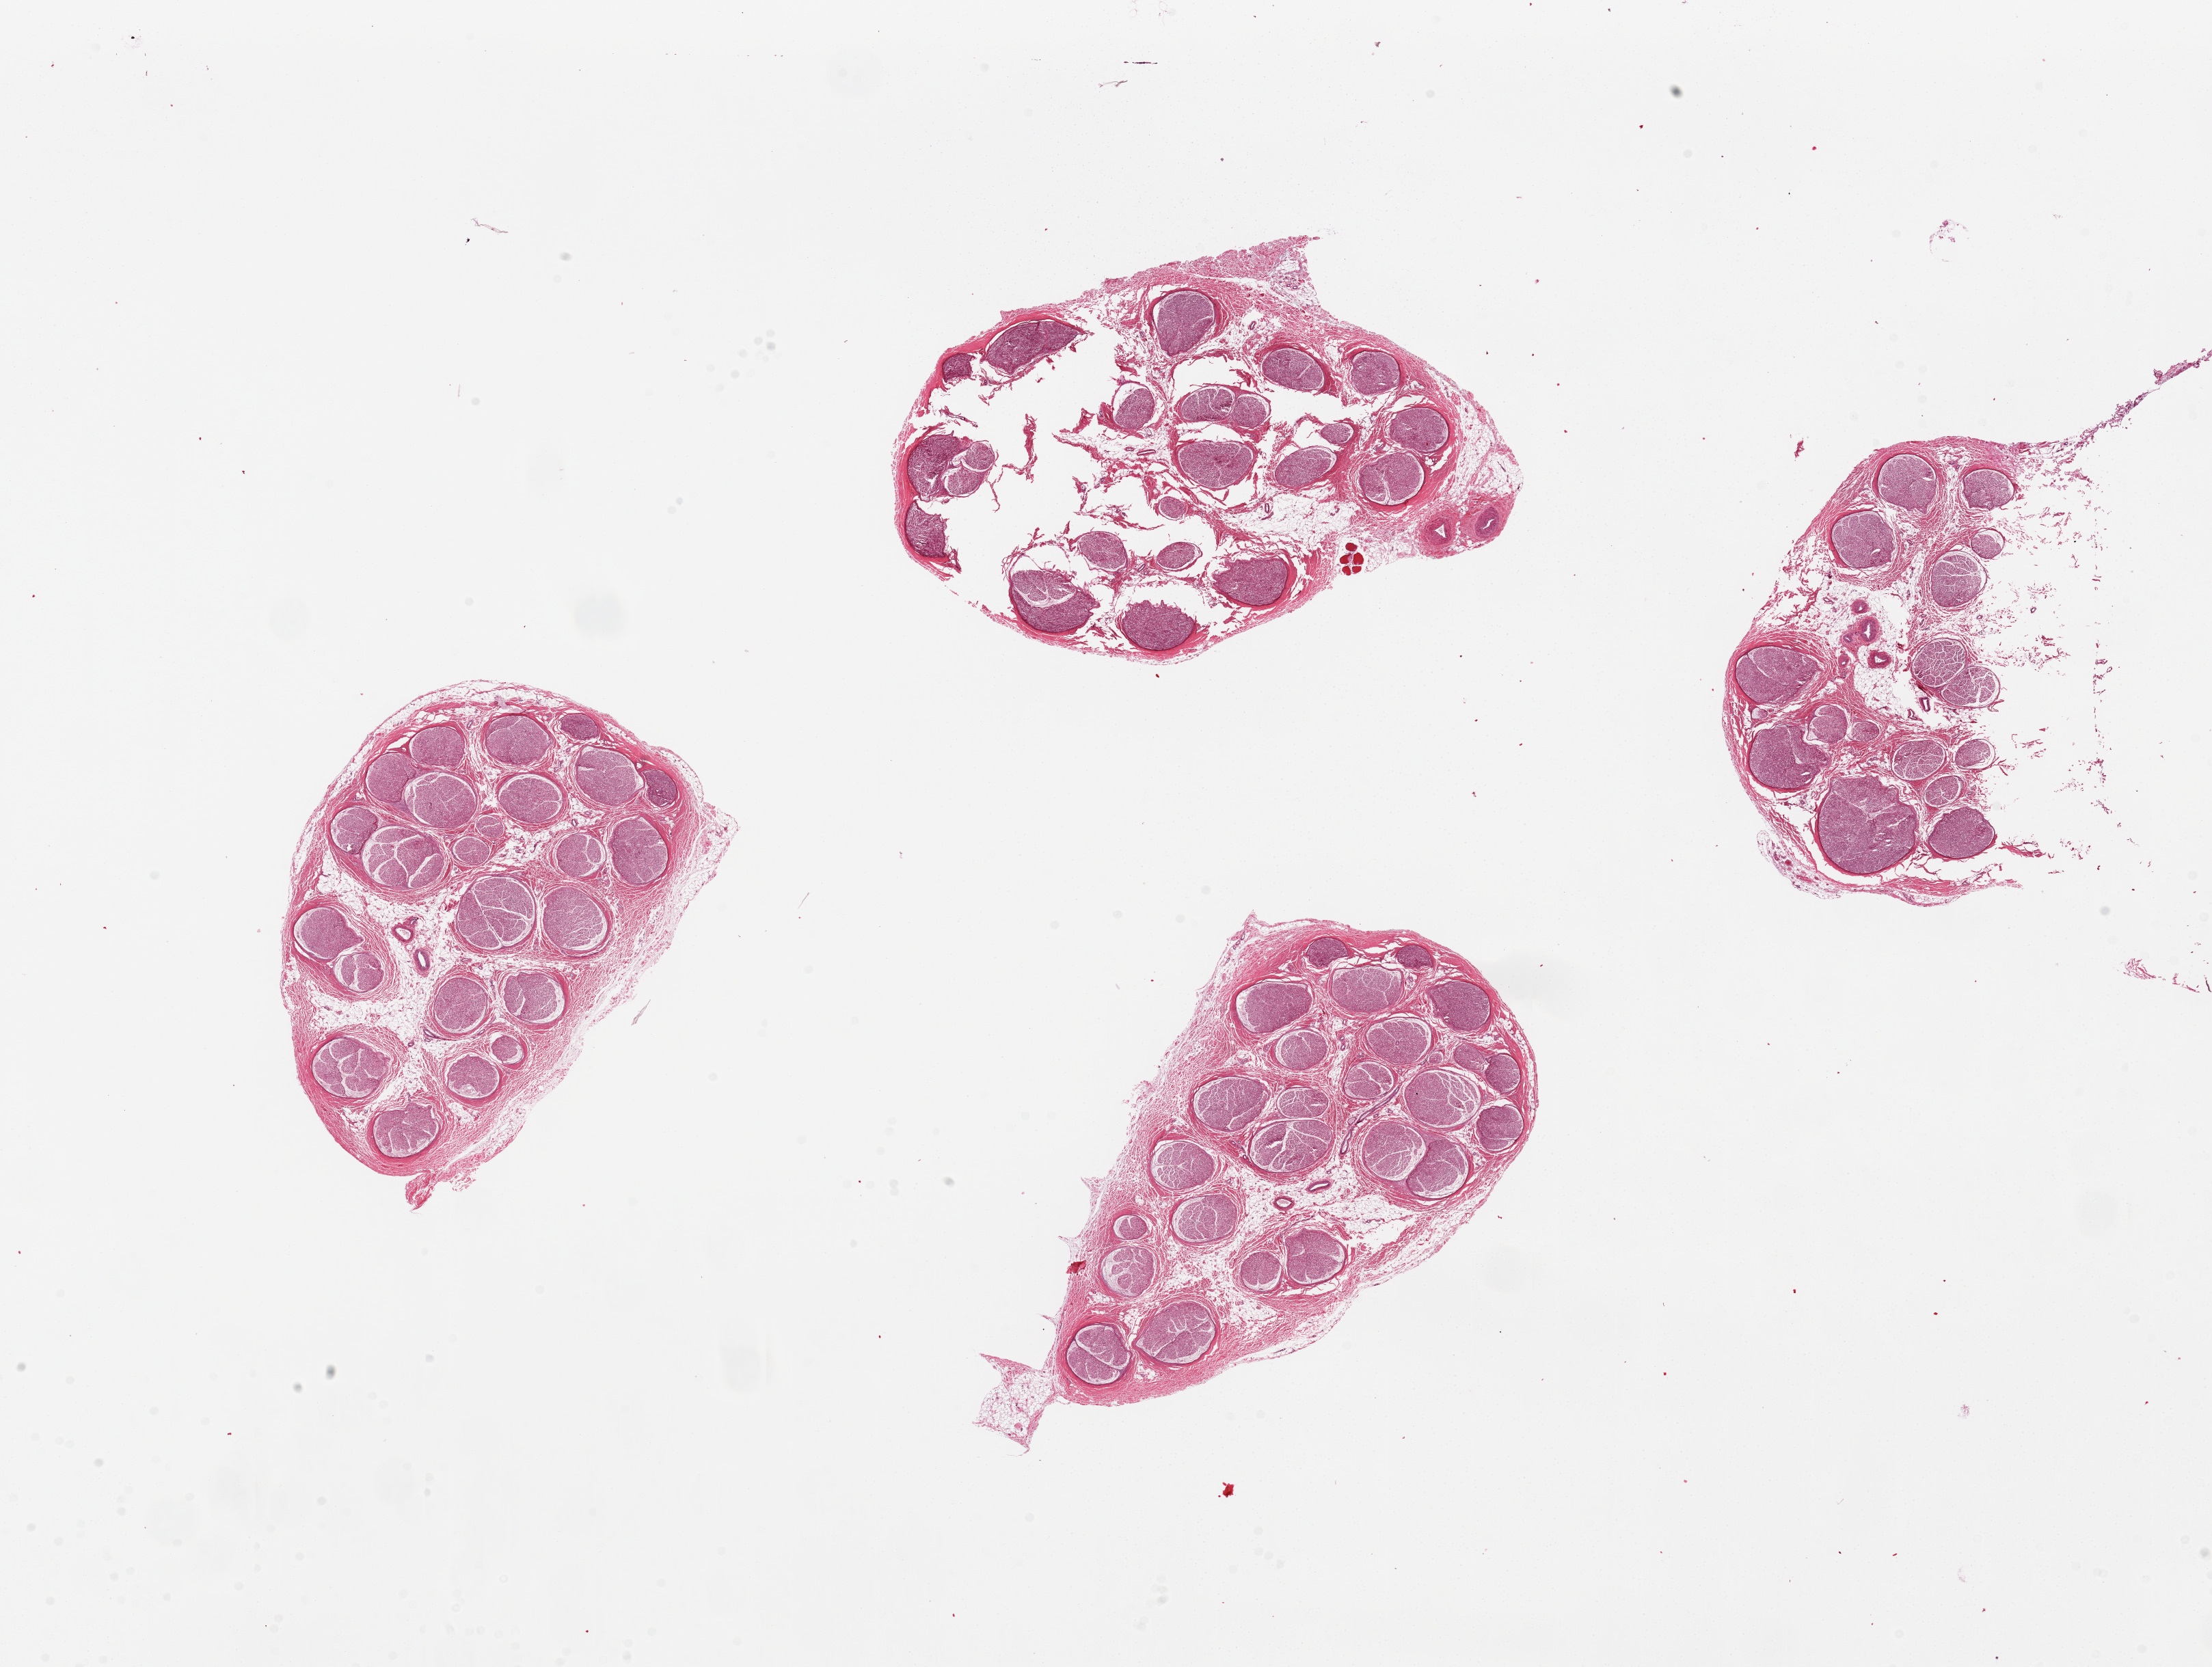
Digitized haematoxylin and eosin-stained section, brightfield — a low-resolution overview of the entire scanned area, about 25.6 x 19.3 mm, PAXgene-fixed, paraffin-embedded tissue, section of tibial nerve (target tissue), donor tissue sample. Donor: male.
Pathologist's review note for this sample: 4 pieces, clean specimens; minute adherent nubbin of fat or vessel on 2.